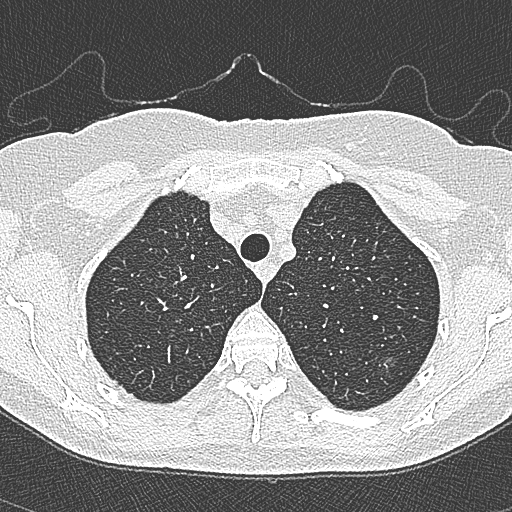
Chest CT (low-dose screening protocol), one axial image. Second screening round (one year after baseline). Lung window (W 1500 / L -600 HU). 1 mm slice thickness. Lung (sharp) reconstruction kernel (B80f). 120 kVp. 512 × 512 image matrix. Female participant, aged 65 years at enrolment.
• Lesion marked by an expert reader, bounding box (x1, y1, x2, y2) in pixels: (364, 350, 404, 385).
• The screening reader recorded 4 non-calcified nodules or masses ≥4 mm on this exam; which of them this box marks is not recorded.
• Official screen result: positive, change unspecified: nodule(s) >= 4 mm or enlarging nodule(s), mass(es), or other non-specific abnormalities suspicious for lung cancer.
• Lung cancer was diagnosed 54 days after this screen: bronchiolo-alveolar carcinoma, non-mucinous, left upper lobe, stage IA (AJCC 6th edition), 10 mm at pathology.